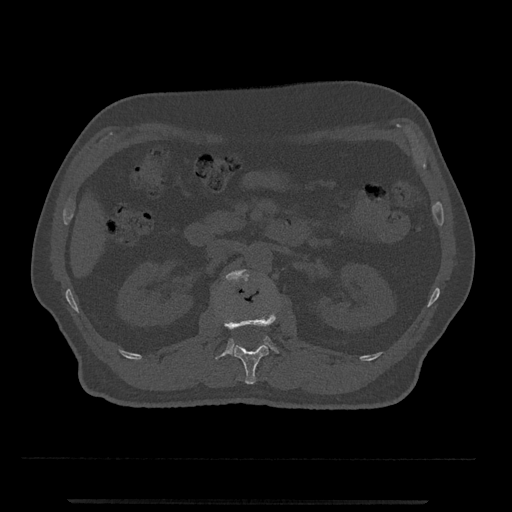
CT including the spine, one axial slice. Position 307 of 797 along the scan axis. Reconstruction kernel Br40s/3. 120 kVp. Bone window (W 1800 / L 400 HU). 0.5 mm slice thickness. 512 × 512 image matrix, field of view 419 × 419 mm. Patient: male, 63 years. From the clinical record (not read from this slice): primary cancer: prostate.
Outlined on this slice (semi-automatically segmented with operator editing):
- L1 vertebra: bounding box <223,312,277,384> (left, top, right, bottom; pixels)
- L2 vertebra: <216,269,278,359>